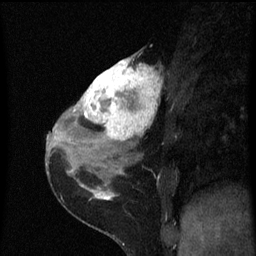
Breast MRI (dynamic contrast-enhanced), one sagittal slice; dynamic contrast-enhanced series, image 2 of 3 at this slice position (ordered by acquisition); 1.5 T; TE 4.2 ms, TR 8 ms; 256 × 256 image matrix, field of view 180 × 180 mm. Female patient, age 38 years.
Structures marked on this image (semi-automatic segmentation, software-assisted and operator-edited):
- analysis volume of interest (the breast-tissue region the enhancement analysis was run in; not a lesion): bounding box [x1, y1, x2, y2] px = [80, 54, 161, 151]
- tumour enhancement mask (voxels above the 70 % enhancement threshold inside the analysis volume of interest): [80, 58, 161, 143]